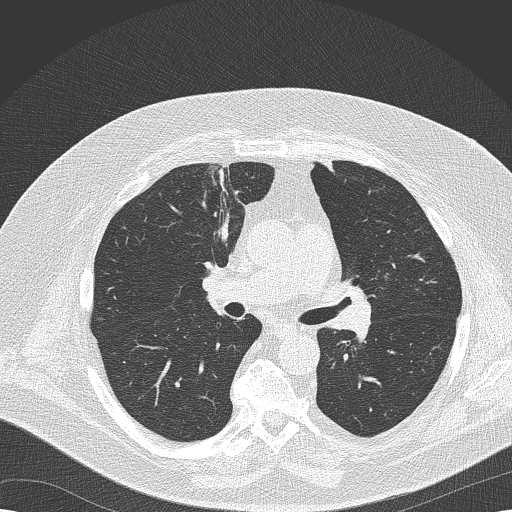
Low-dose screening chest CT, axial slice. Second screening round (one year after baseline). Lung window (W 1500 / L -600 HU). 2 mm slice thickness. Lung (sharp) reconstruction kernel (B50f). 512 × 512 image matrix. Male participant, aged 68 years at enrolment. Former smoker at enrolment.
- Expert-annotated lung lesion, bounding box [x1, y1, x2, y2] px = [319, 260, 388, 322].
- Screening reader's record for this exam (one nodule recorded; not confirmed to be the boxed lesion): non-calcified nodule or mass ≥4 mm, left lower lobe, 8 × 6 mm, soft tissue attenuation, pre-existing on the prior screen: yes; interval growth: no.
- Later outcome: lung cancer diagnosed 256 days after this screen — squamous cell carcinoma, NOS, left upper lobe, poorly differentiated (G3), stage IIB (AJCC 6th edition), 35 mm at pathology.